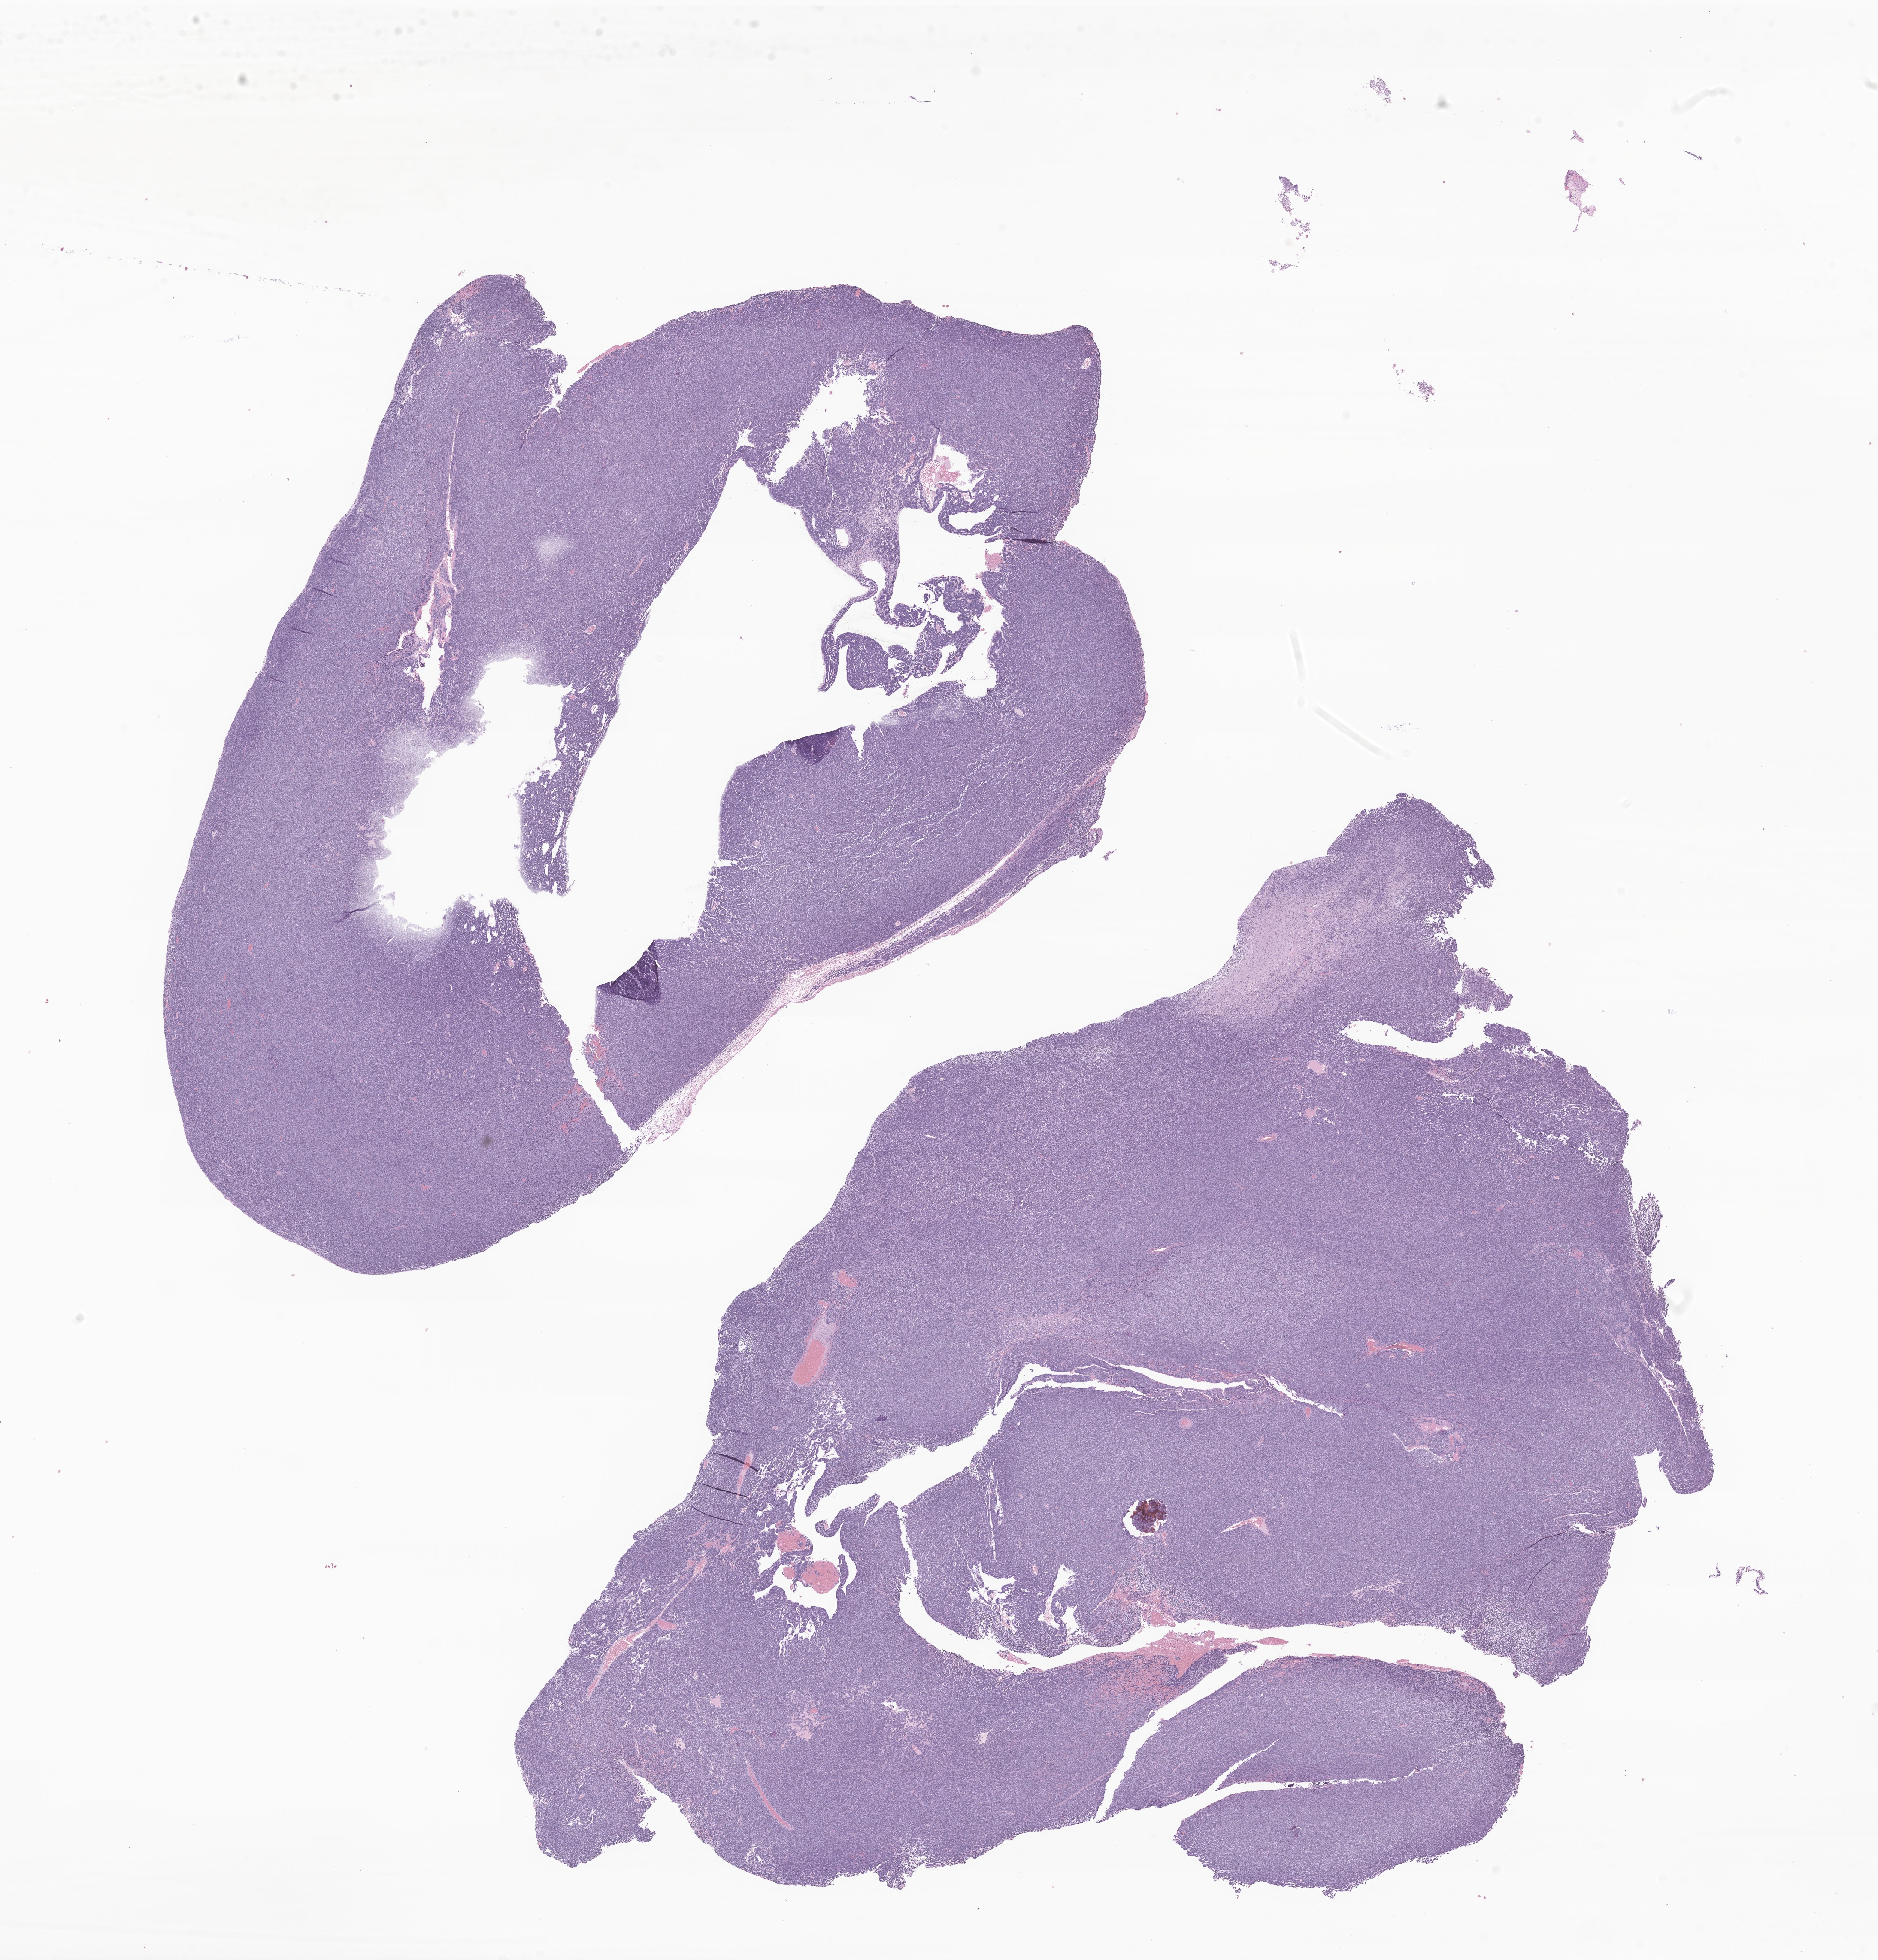
H&E whole-slide image of tumor tissue from the brain — shown as a low-resolution overview of the whole scanned area (about 21.1 x 22.1 mm). Formalin-fixed, paraffin-embedded (FFPE) tissue. Patient: male, age 65 months.
- diagnosis: Tumor cells, uncertain whether benign or malignant